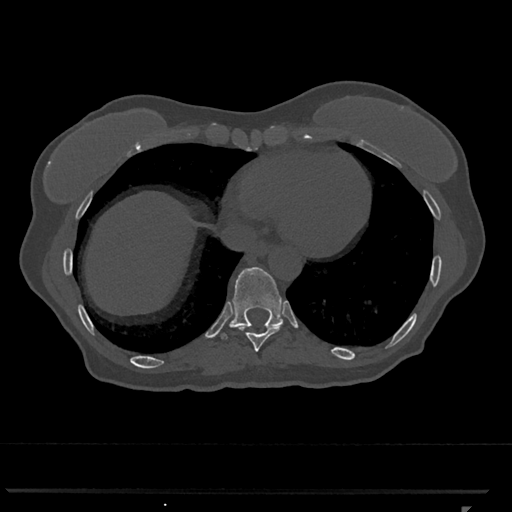
CT including the spine, one axial slice. Position 593 of 793 along the scan axis. Reconstruction kernel Br40s/3. Bone window (W 1800 / L 400 HU). 0.5 mm slice thickness. 512 × 512 image matrix. Female patient, age 62 years. Case-level facts recorded for this patient, not image findings: primary cancer: renal.
Annotated regions visible in this slice (semi-automatically segmented with operator editing):
- T10 vertebra: box from (x=221, y=267) to (x=283, y=339) px
- T9 vertebra: (x=238, y=324)–(x=283, y=352)